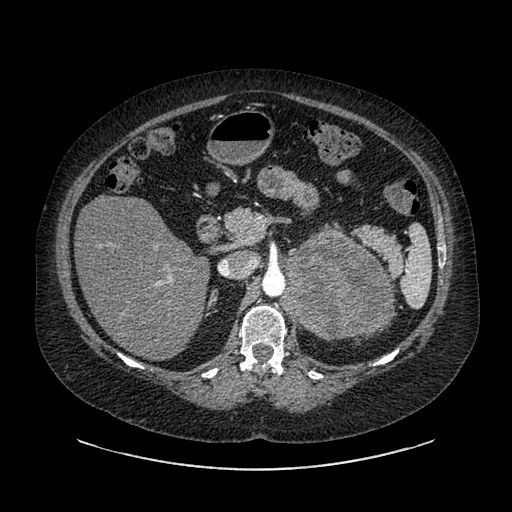
Contrast-enhanced abdominal CT, one axial slice. Slice 563 of 769 in the series (ordered by position). Reconstruction kernel SOFT. Soft-tissue window (W 400 / L 40 HU). 0.62 mm slice thickness. 512 × 512 image matrix. Patient: female, 61 years. Case-level facts recorded for this patient, not image findings: diagnosis: adrenocortical carcinoma; tumour side: left adrenal; tumour size at pathology: 13 cm; Ki-67 index: 79 %.
Structures marked on this image (semi-automatic segmentation, software-assisted and operator-edited):
- mass: bounding box <282,230,391,340> (left, top, right, bottom; pixels)